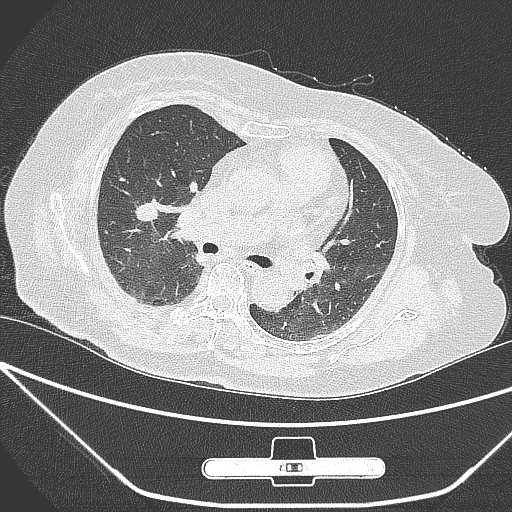
Chest CT, one axial slice. Slice 157 of 245 in the series (ordered by position). 120 kVp. Lung window (W 1500 / L -600 HU). 1 mm slice thickness. 512 × 512 image matrix, field of view 365 × 365 mm. Patient: female, 65 years. From the clinical record (not read from this slice): clinical TNM (as recorded): T1c N0 M0.
Outlined on this slice (bounding box drawn by a radiologist):
- lung tumour (recorded histology: adenocarcinoma): bounding box [x1, y1, x2, y2] px = [135, 195, 159, 233]